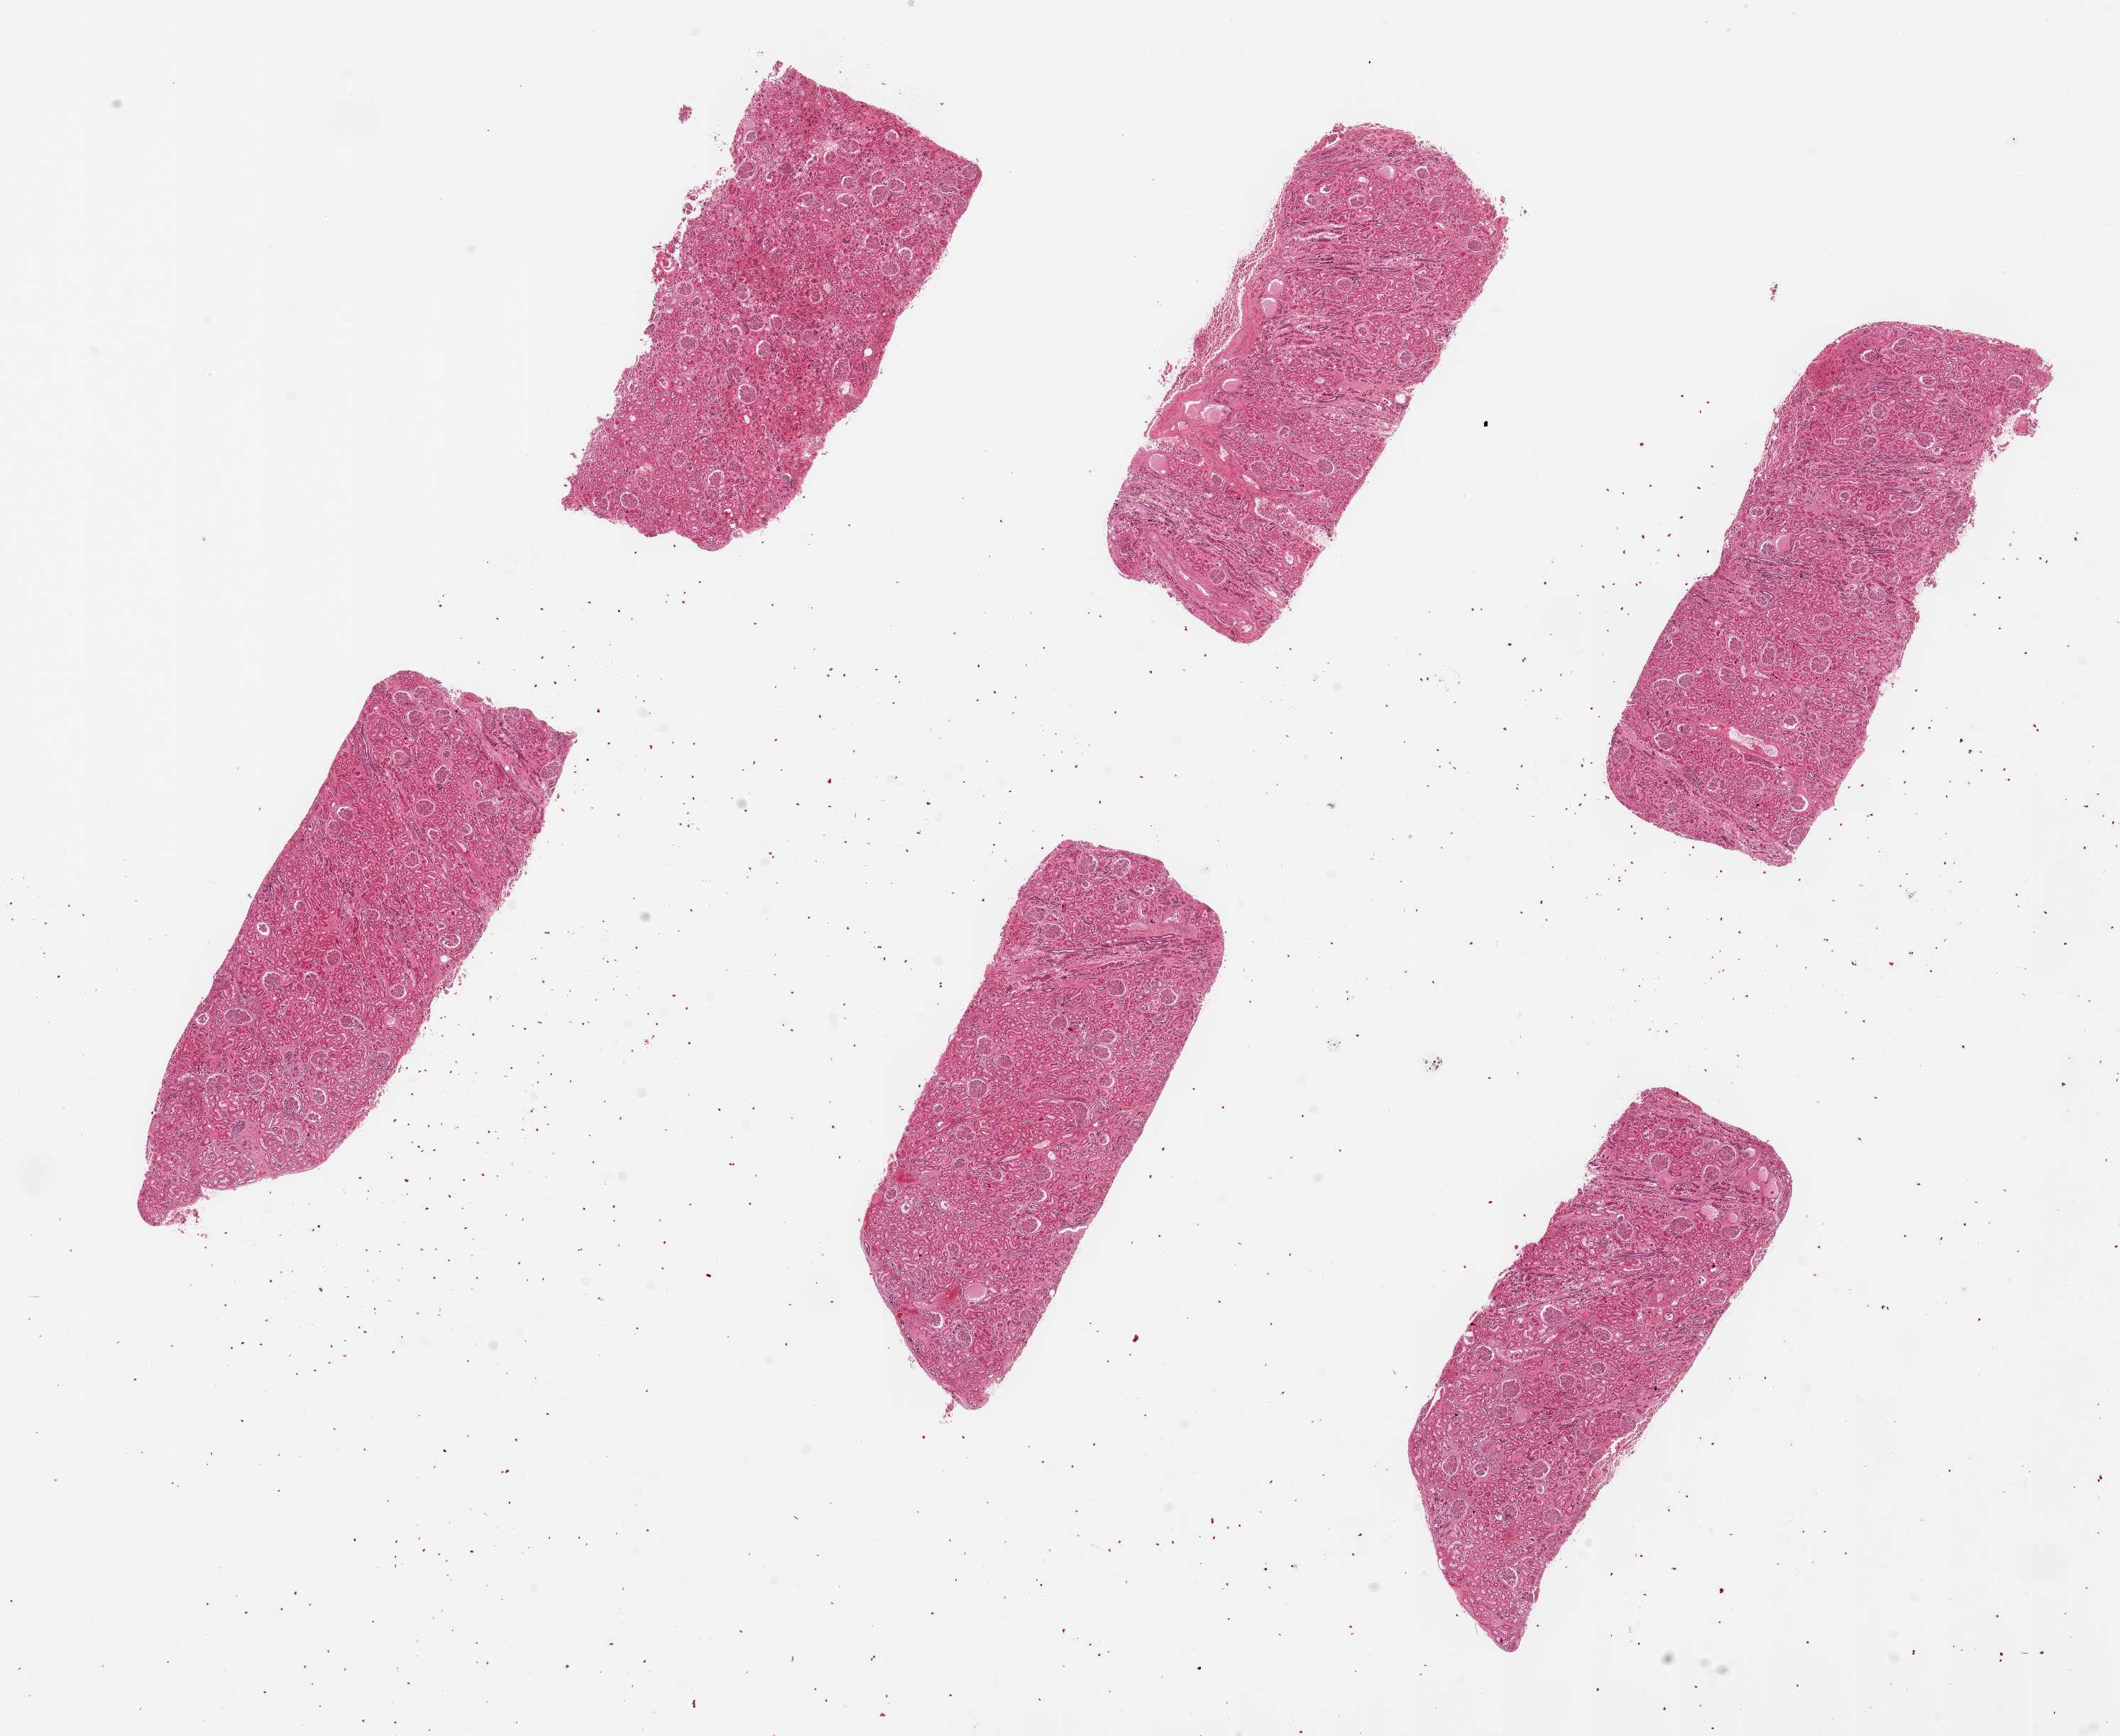
H&E whole-slide image — whole scanned area (about 23.6 x 19.3 mm) shown as a low-resolution overview. PAXgene-fixed, paraffin-embedded tissue. Section of renal cortex (target tissue). Donor tissue sample.
Reviewer comment on this tissue sample: 6 pieces. up to 7x2.5mm glomeruli well visualized.